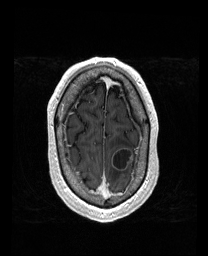
Brain MRI from a brain-tumour surgery series, one axial slice; slice 149 of 192 in the series (ordered by position); T1-weighted post-contrast; 1 mm slice thickness; 208 × 256 image matrix, field of view 211 × 260 mm. From the clinical record (not read from this slice): histopathology: Metastatic Carcinoma from Lung Adenocarcinoma; tumour location: Left Frontal.
Annotated regions visible in this slice (expert manual segmentation):
- tumour: bounding box [x1, y1, x2, y2] px = [113, 147, 133, 171]